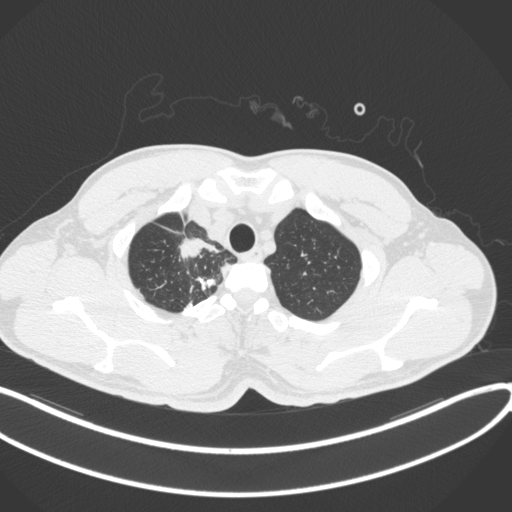
Chest CT, one axial slice; slice 331 of 391 in the series (ordered by position); reconstruction kernel B31f; 120 kVp; lung window (W 1500 / L -600 HU); 512 × 512 image matrix, field of view 400 × 400 mm. Male patient, age 48 years. Case-level facts recorded for this patient, not image findings: clinical TNM (as recorded): T1c N1 M1.
Annotated regions visible in this slice (rectangle marked by the reading radiologist):
- lung tumour (recorded histology: adenocarcinoma): bounding box (x1, y1, x2, y2) in pixels: (177, 232, 222, 264)